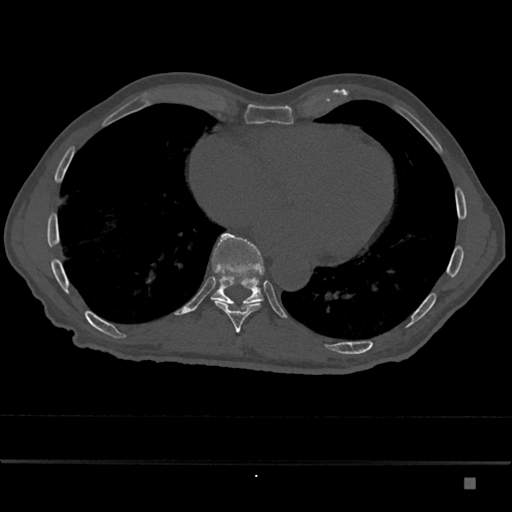
CT including the spine, one axial slice. Slice 779 of 797 in the series (ordered by position). Reconstruction kernel Br40s/3. Bone window (W 1800 / L 400 HU). 0.5 mm slice thickness. 512 × 512 image matrix, field of view 390 × 390 mm. Patient: male, 72 years. Case-level facts recorded for this patient, not image findings: primary cancer: prostate.
Outlined on this slice (semi-automatically segmented with operator editing):
- T10 vertebra: box from (x=211, y=233) to (x=265, y=308) px
- T9 vertebra: (x=214, y=301)–(x=261, y=333)